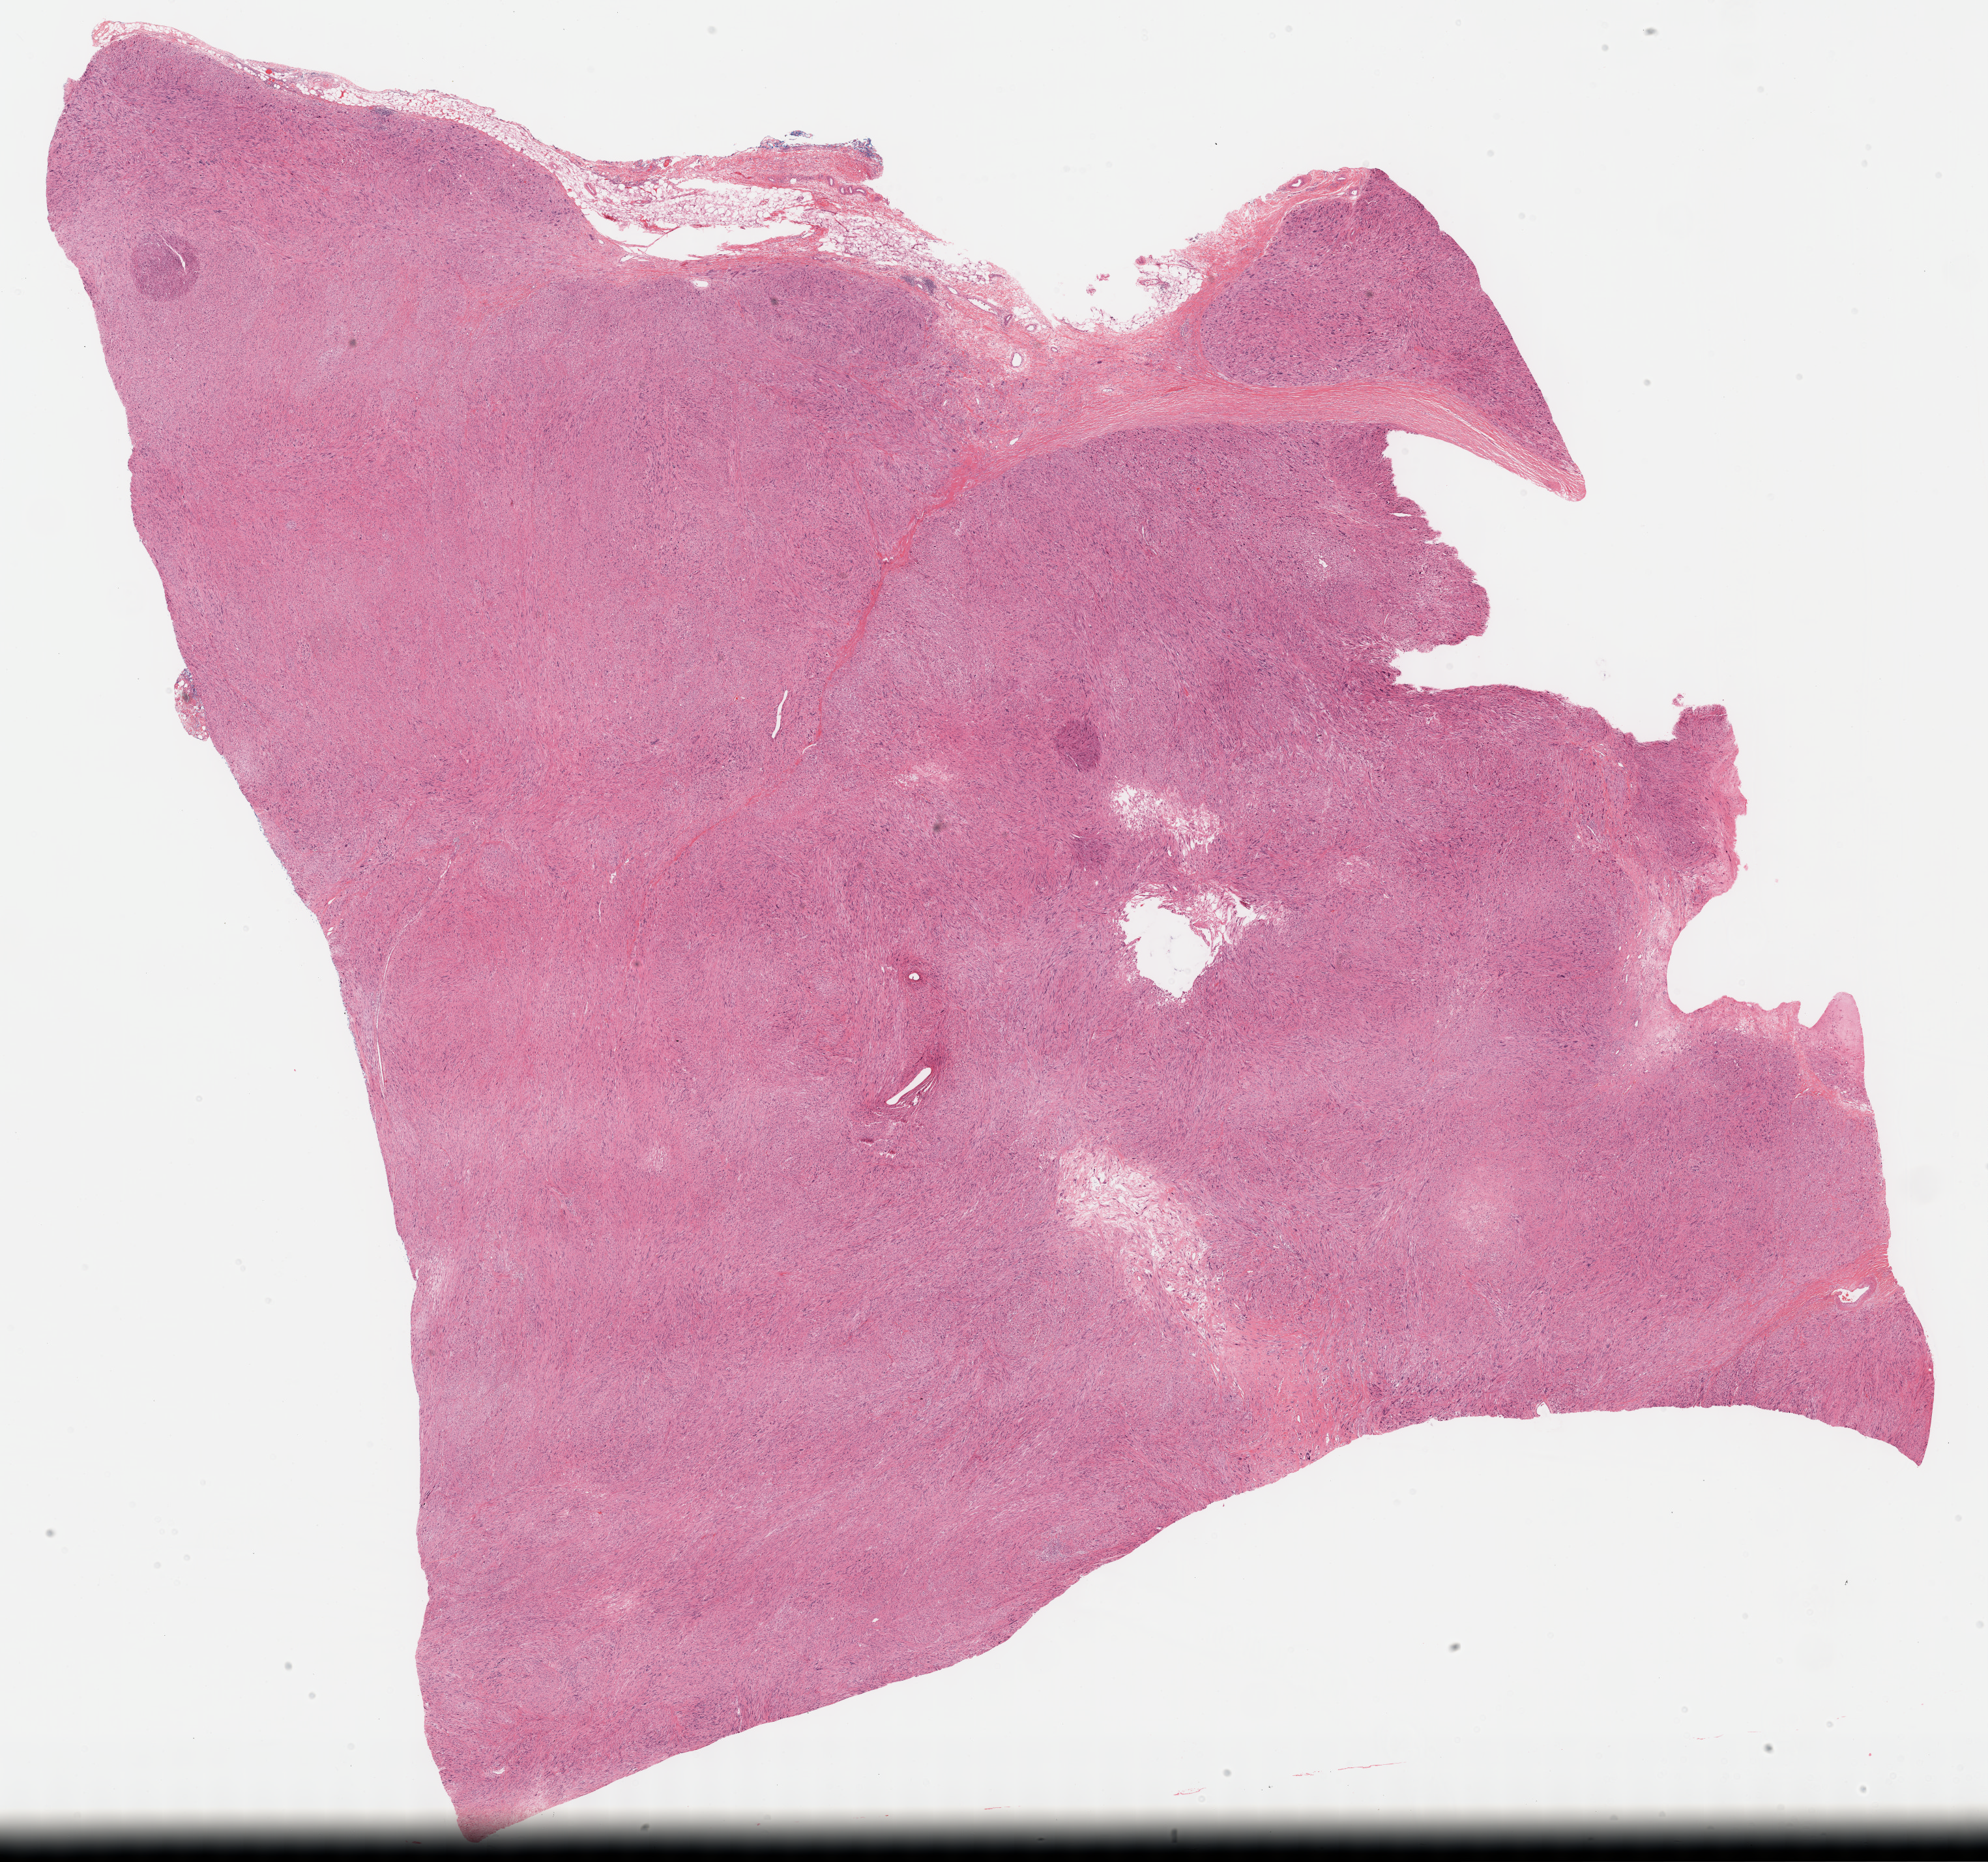
Whole-slide histology image, H&E-stained — a low-resolution overview of the entire scanned area, about 24.7 x 23.1 mm (slide scanned at 40x), formalin-fixed paraffin-embedded (FFPE) diagnostic section, retroperitoneum and peritoneum, primary tumour sample. Male, age 41 years at initial diagnosis.
Diagnosis: Leiomyosarcoma, NOS (retroperitoneum).